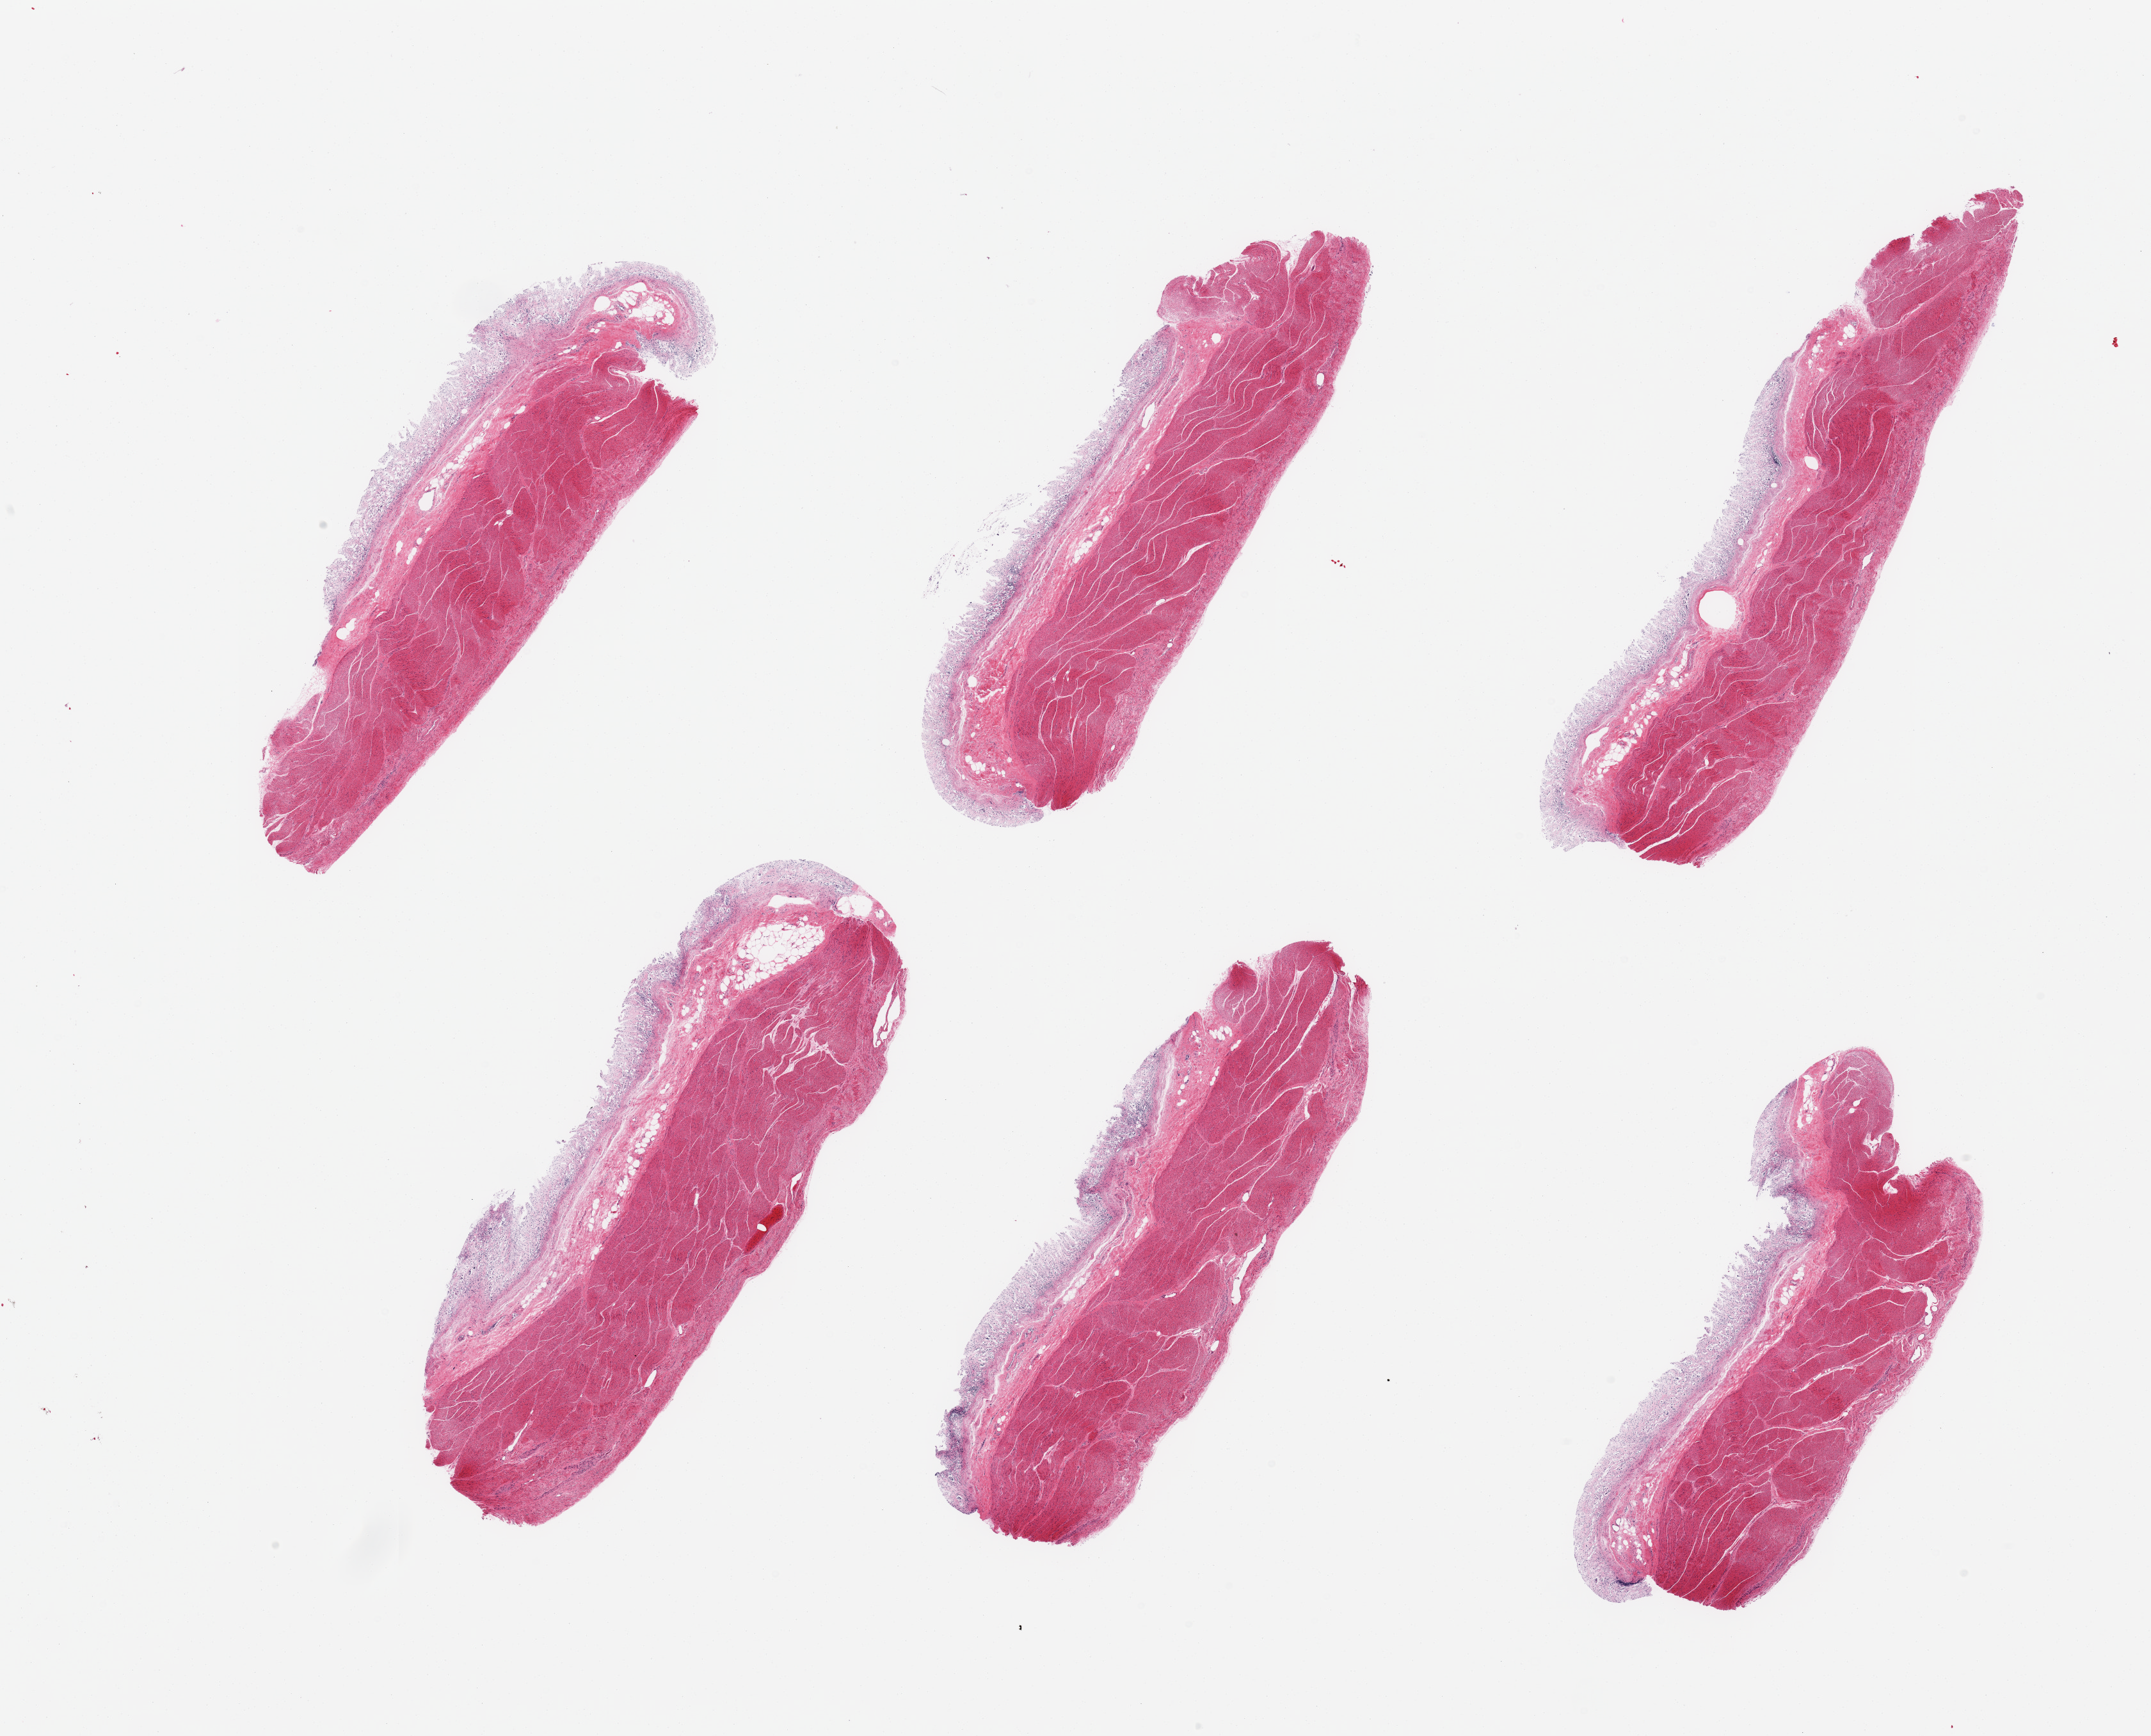
Whole-slide image, H&E stain — whole scanned area (about 26.6 x 21.5 mm, slide scanned at 20x) shown as a low-resolution overview; PAXgene-fixed, paraffin-embedded tissue; target tissue: stomach; tissue donor sample. Donor: male.
Reviewer comment on this tissue sample: 6 pieces; severely autolyzed gastric mucosa and preserved muscularis.